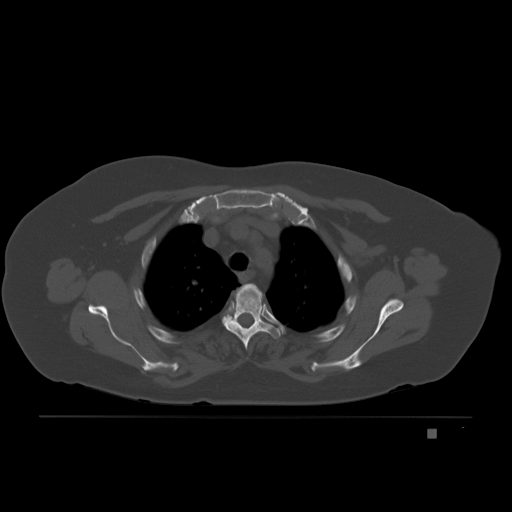
CT including the spine, one axial slice. Slice 160 of 221 in the series (ordered by position). Bone window (W 1800 / L 400 HU). 3 mm slice thickness. 512 × 512 image matrix, field of view 474 × 474 mm. Female patient, age 63 years. From the clinical record (not read from this slice): primary cancer: breast.
Annotated regions visible in this slice (semi-automatic segmentation, software-assisted and operator-edited):
- T3 vertebra: box from (x=222, y=284) to (x=280, y=350) px